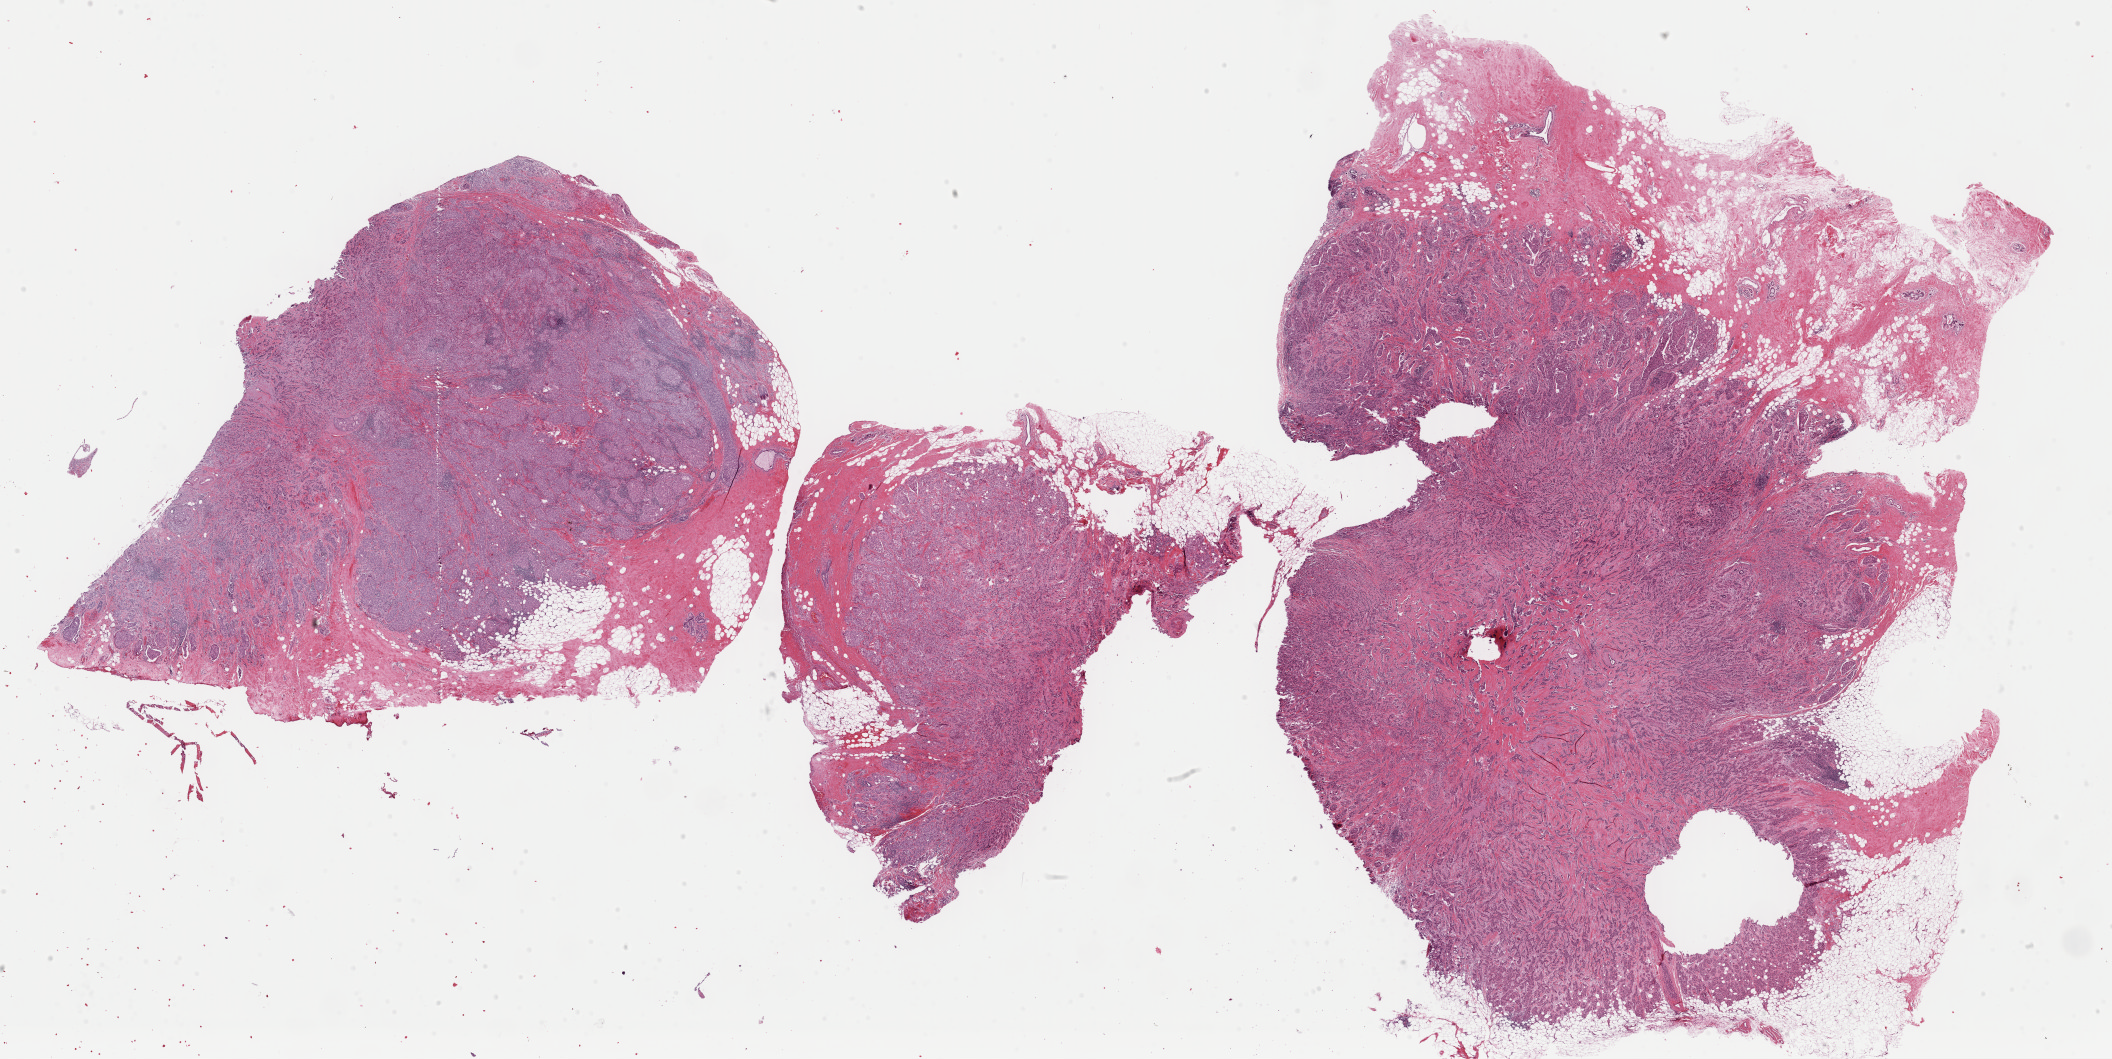
H&E whole-slide image — low-resolution overview of the scanned area, about 33.4 x 16.7 mm (acquisition: 40x scan); FFPE section; primary tumour sample from the breast. Female, age 54 years at initial diagnosis.
Diagnosis: Infiltrating duct carcinoma, NOS. AJCC pathologic stage: I (6th edition). Laterality: left. Lymph nodes positive (case pathology): 0 of 4 examined.